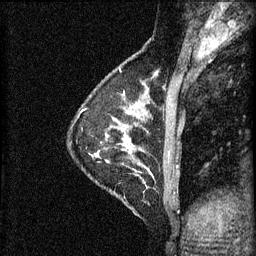
Breast MRI (dynamic contrast-enhanced), one sagittal slice. Slice 18 of 60 in the series (ordered by position). 3 images stored at this slice position (order not interpretable as contrast timing). 1.5 T. TE 4.2 ms, TR 11 ms. 2 mm slice thickness. 256 × 256 image matrix, field of view 180 × 180 mm. Patient: female, 29 years.
Outlined on this slice (semi-automatic segmentation, software-assisted and operator-edited):
- analysis volume of interest (the breast-tissue region the enhancement analysis was run in; not a lesion): bounding box (x1, y1, x2, y2) in pixels: (106, 172, 171, 219)
- tumour enhancement mask (voxels above the 70 % enhancement threshold inside the analysis volume of interest): (140, 172, 154, 177)